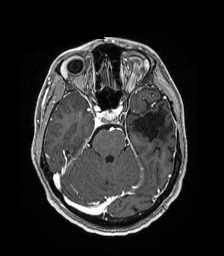
Brain MRI from a brain-tumour surgery series, one axial slice; slice 120 of 192 in the series (ordered by position); T1-weighted post-contrast; 1 mm slice thickness; 224 × 256 image matrix. From the clinical record (not read from this slice): histopathology: Low grade glioma; IDH mutation: no; tumour location: Left Parieto-Occipital Intraventricular.
Annotated regions visible in this slice (outlined manually by an expert reader):
- previous resection cavity: bounding box [x1, y1, x2, y2] px = [133, 110, 164, 141]